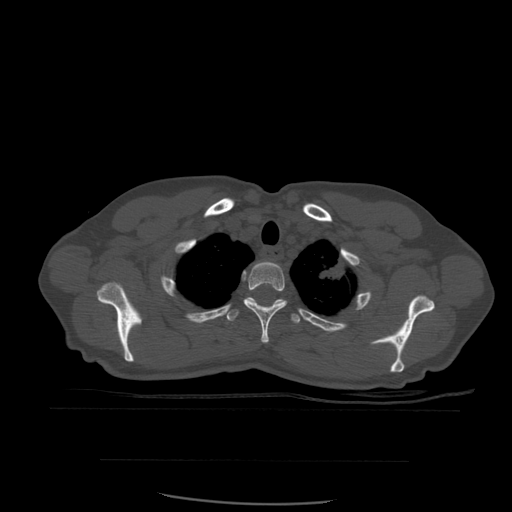
CT including the spine, one axial slice. Position 454 of 574 along the scan axis. Bone window (W 1800 / L 400 HU). 1.25 mm slice thickness. 512 × 512 image matrix, field of view 392 × 392 mm. Patient age 48 years. Case-level facts recorded for this patient, not image findings: primary cancer: lung.
Annotated regions visible in this slice (semi-automatically segmented with operator editing):
- T2 vertebra: bounding box <244,261,287,344> (left, top, right, bottom; pixels)
- T3 vertebra: <224,297,303,324>